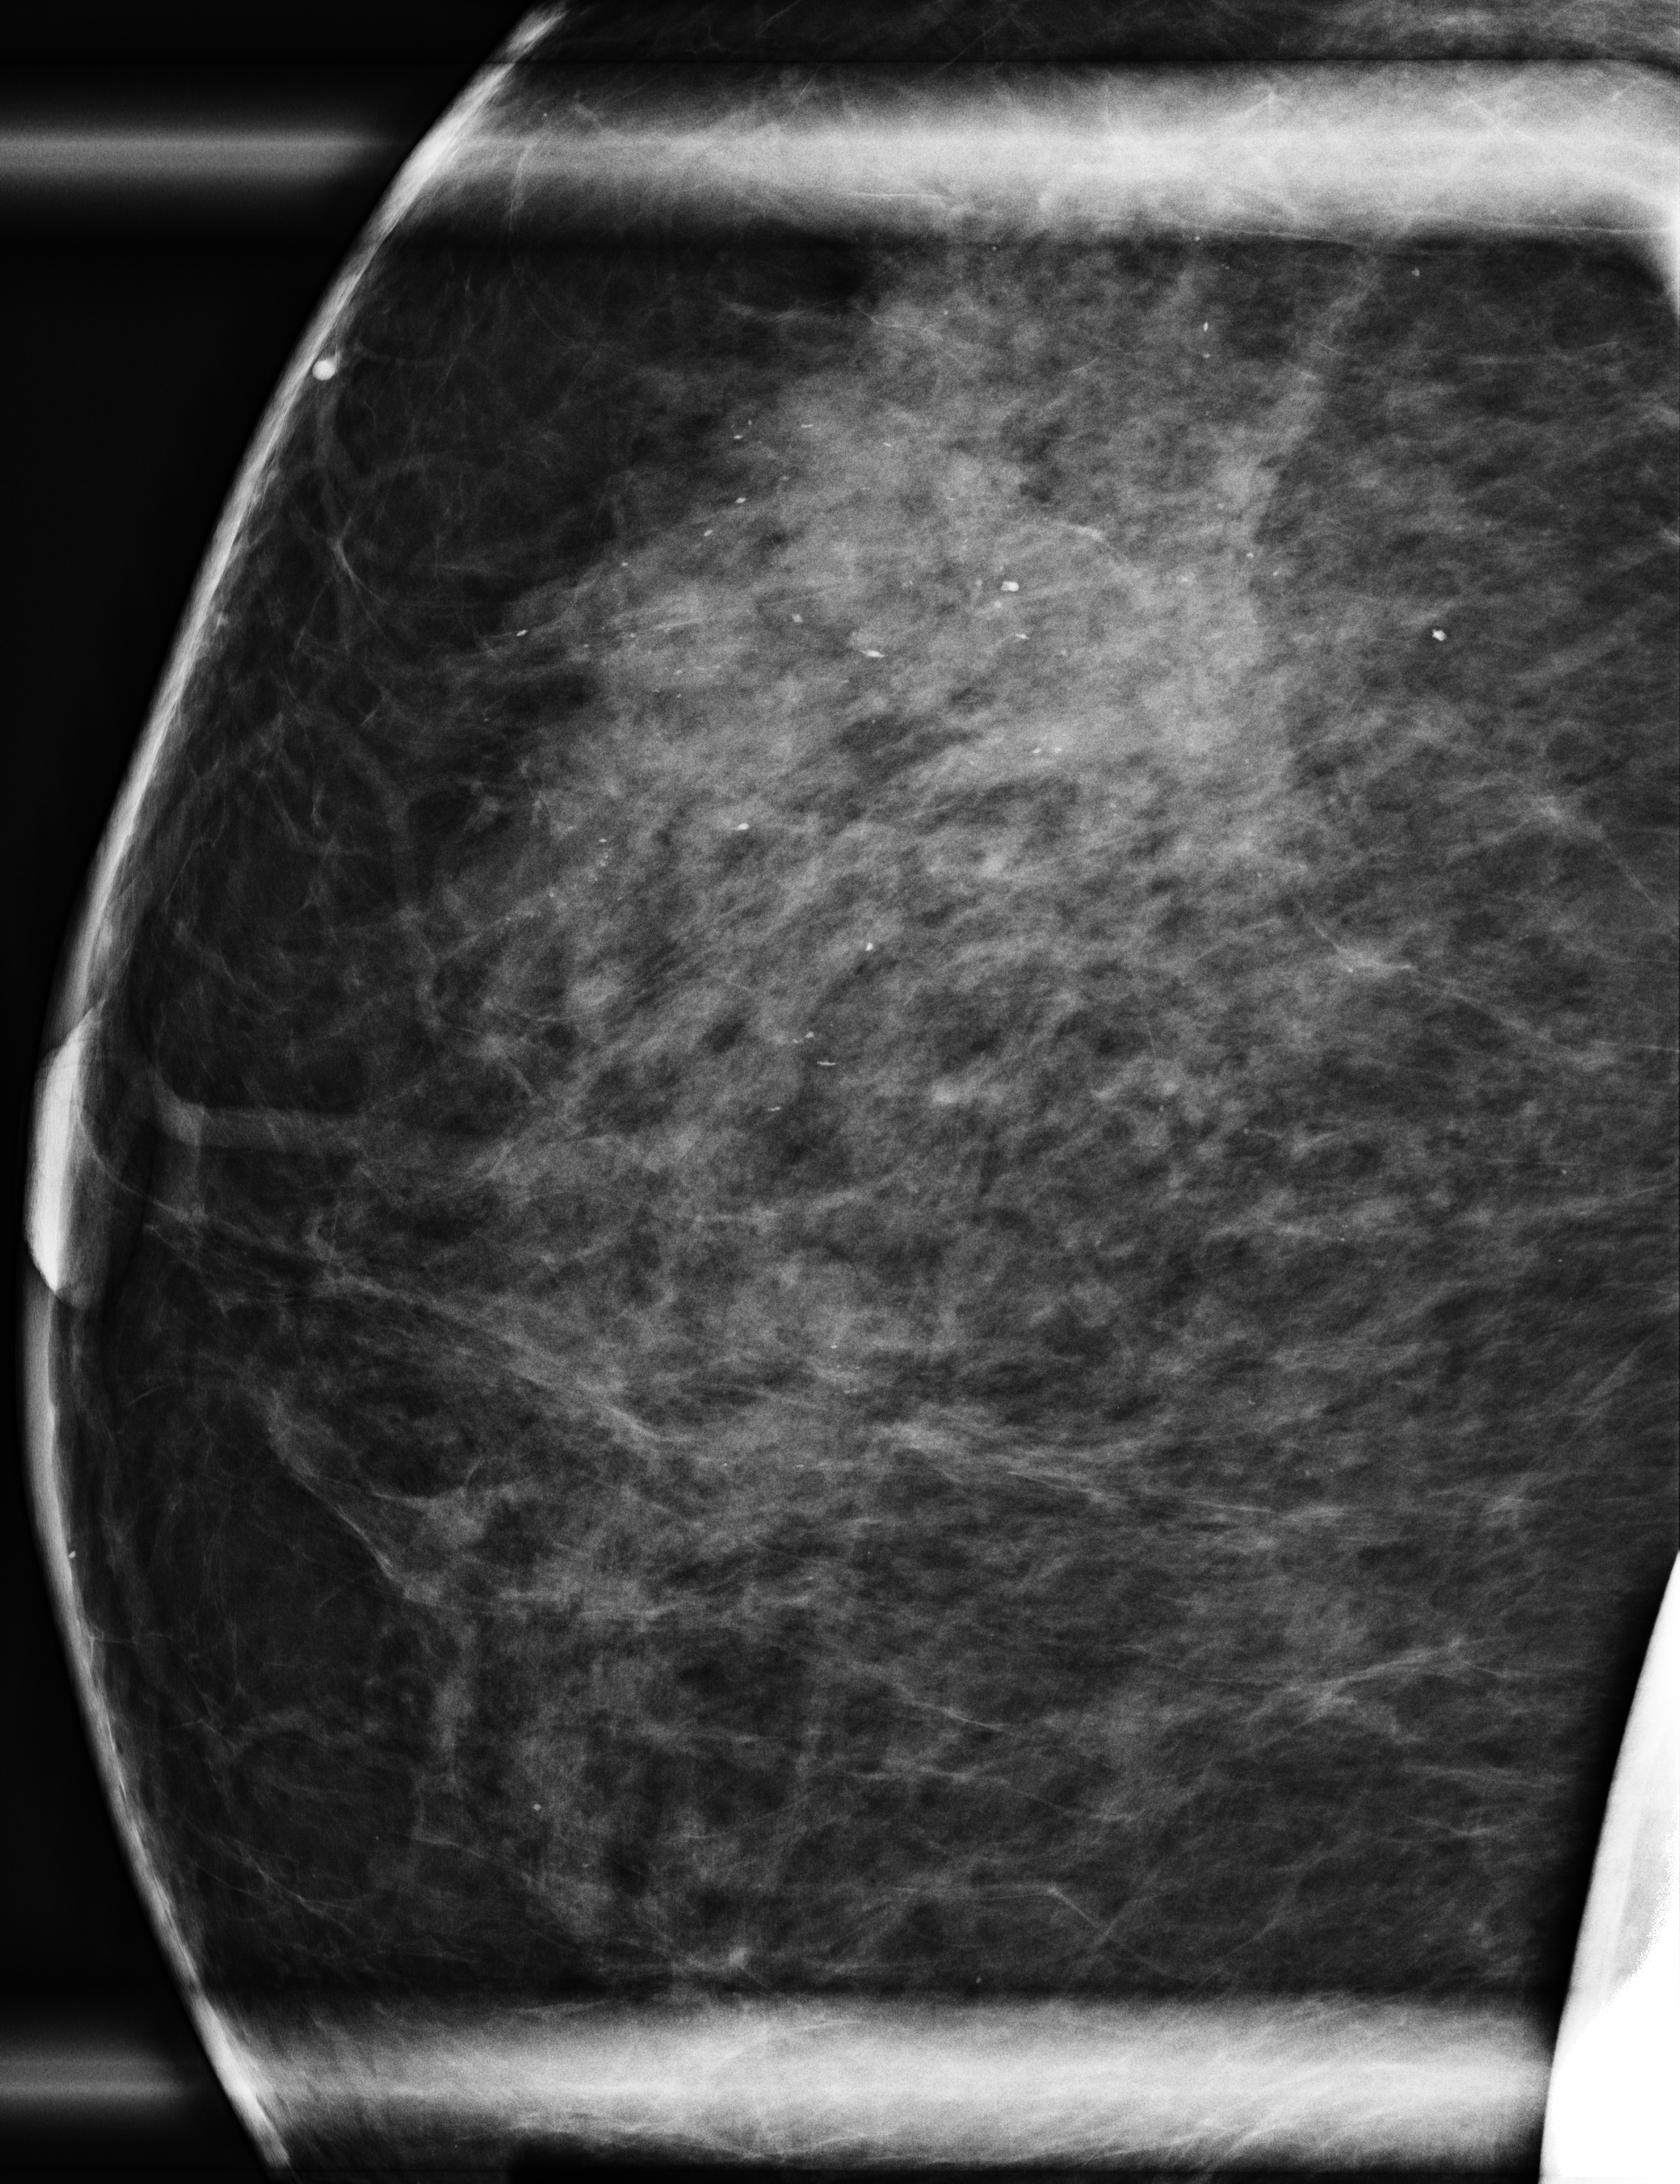
Additional (diagnostic) view. Patient: female, 71 years.
Image type: full-field digital mammogram. Breast: right. Projection: mediolateral (ML) view, magnification. Breast density at the screening exam (both breasts): heterogeneously dense (BI-RADS density category c). Final BI-RADS category for the screening round (tomosynthesis exam, both breasts): category 1. Recall: recalled for additional imaging after this screen.